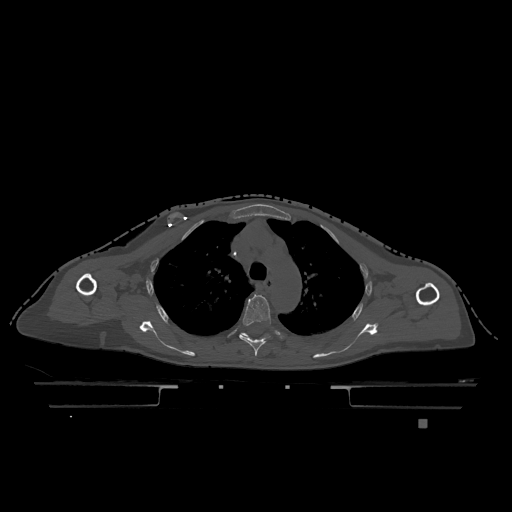
CT including the spine, one axial slice; slice 874 of 1317 in the series (ordered by position); bone window (W 1800 / L 400 HU); 0.5 mm slice thickness; 512 × 512 image matrix. Patient: female, 74 years. Case-level facts recorded for this patient, not image findings: primary cancer: lung; vertebrae with lytic lesions (as recorded): T1, T4, T5, T6, L4, L5.
Annotated regions visible in this slice (semi-automatic segmentation, software-assisted and operator-edited):
- T4 vertebra: bounding box (x1, y1, x2, y2) in pixels: (239, 294, 273, 356)
- T5 vertebra: (240, 333, 248, 337)